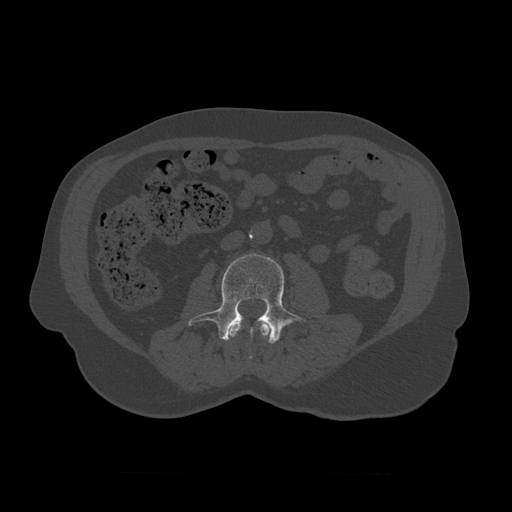
CT including the spine, one axial slice. Position 307 of 450 along the scan axis. Bone window (W 1800 / L 400 HU). 1.25 mm slice thickness. 512 × 512 image matrix, field of view 405 × 405 mm. Patient age 75 years. Case-level facts recorded for this patient, not image findings: primary cancer: prostate.
Outlined on this slice (semi-automatically segmented with operator editing):
- L2 vertebra: bounding box <229,320,271,359> (left, top, right, bottom; pixels)
- L3 vertebra: <188,254,305,344>